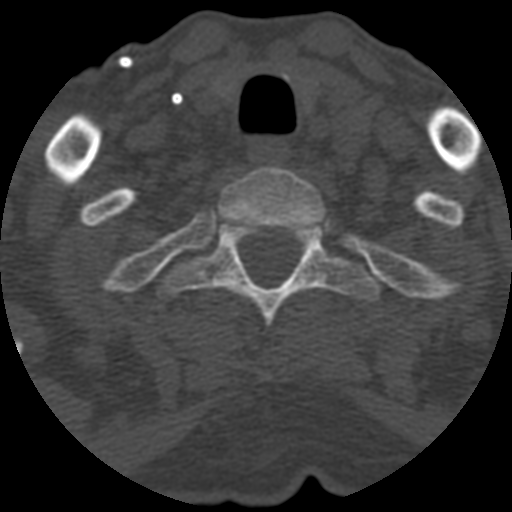
CT including the spine, one axial slice. Slice 509 of 708 in the series (ordered by position). Reconstruction kernel STANDARD. One of 3 acquisitions stored at this slice position. Bone window (W 1800 / L 400 HU). 1.25 mm slice thickness. 512 × 512 image matrix, field of view 160 × 160 mm. Patient age 55 years. From the clinical record (not read from this slice): primary cancer: colon; vertebrae with lytic lesions (as recorded): T12, L1, L5.
Structures marked on this image (semi-automatic segmentation, software-assisted and operator-edited):
- T1 vertebra: bounding box <219,167,324,227> (left, top, right, bottom; pixels)
- T2 vertebra: <156,223,385,327>